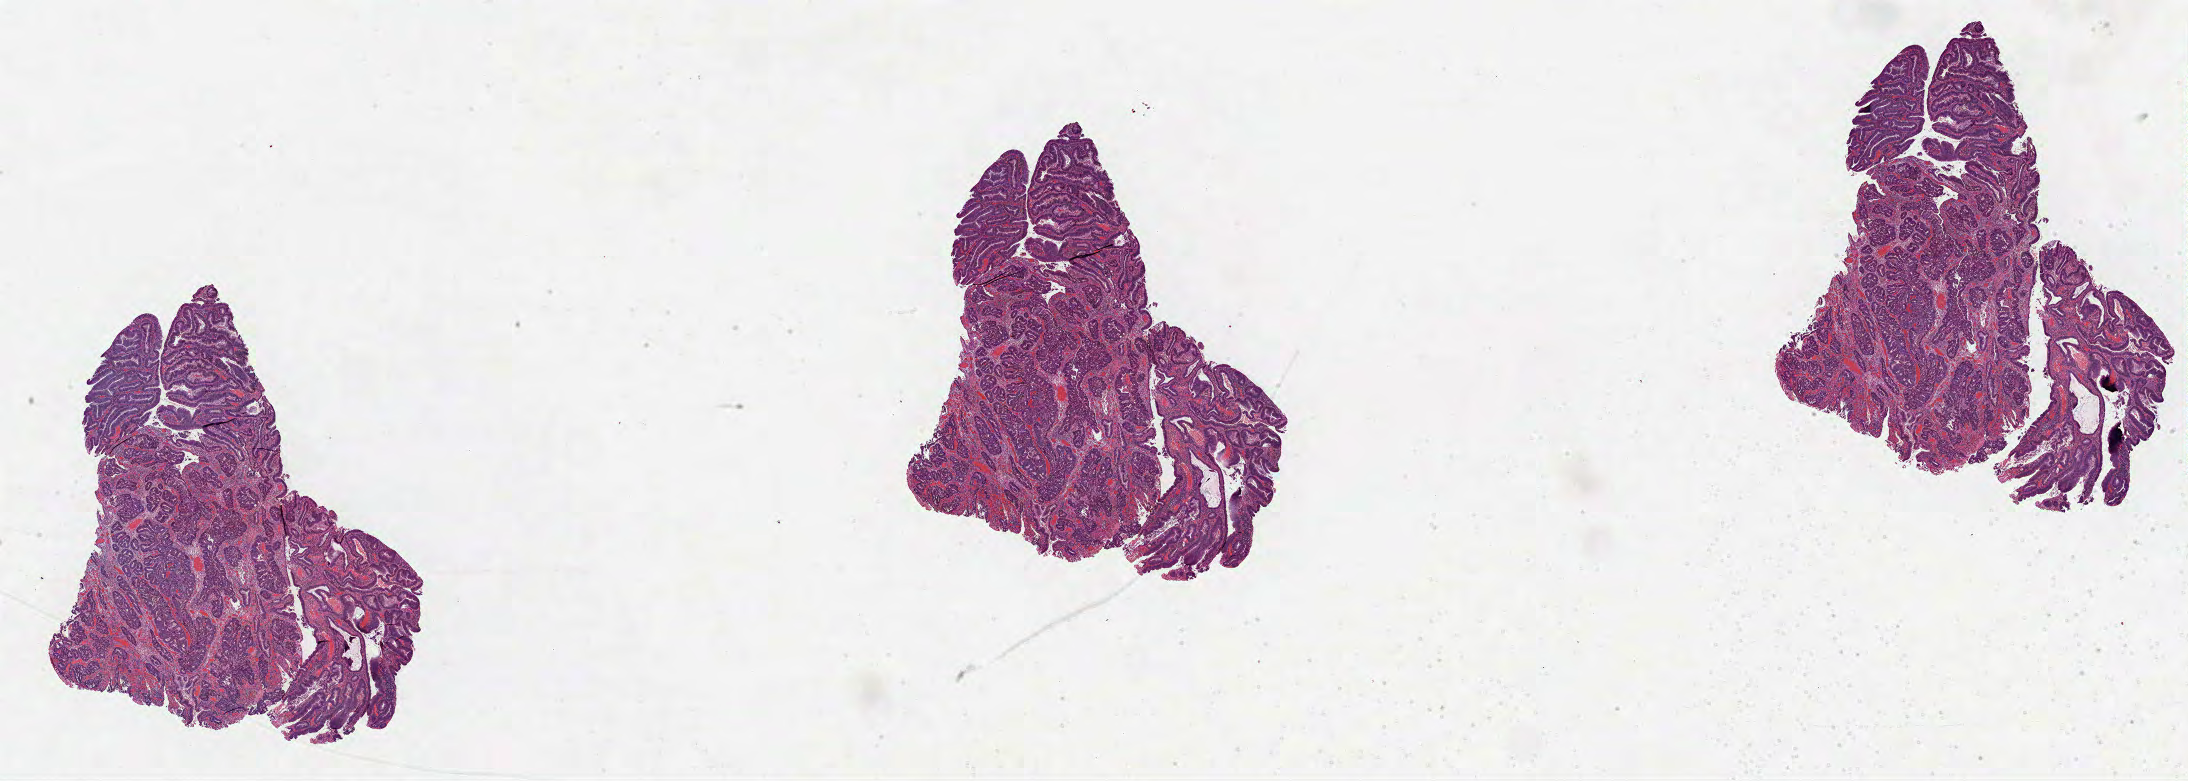
Whole-slide histology image, H&E — low-resolution overview of the scanned area, about 35.3 x 12.6 mm (from a 40x scan), formalin-fixed paraffin-embedded (FFPE) diagnostic section, sample: primary tumour, rectum. Patient: female, age at initial diagnosis 41 years.
TNM: T3 N2 M1. Diagnosis: Adenocarcinoma, NOS (rectosigmoid junction). Lymph nodes positive (case pathology): 6 of 32 examined. AJCC pathologic stage: IV.